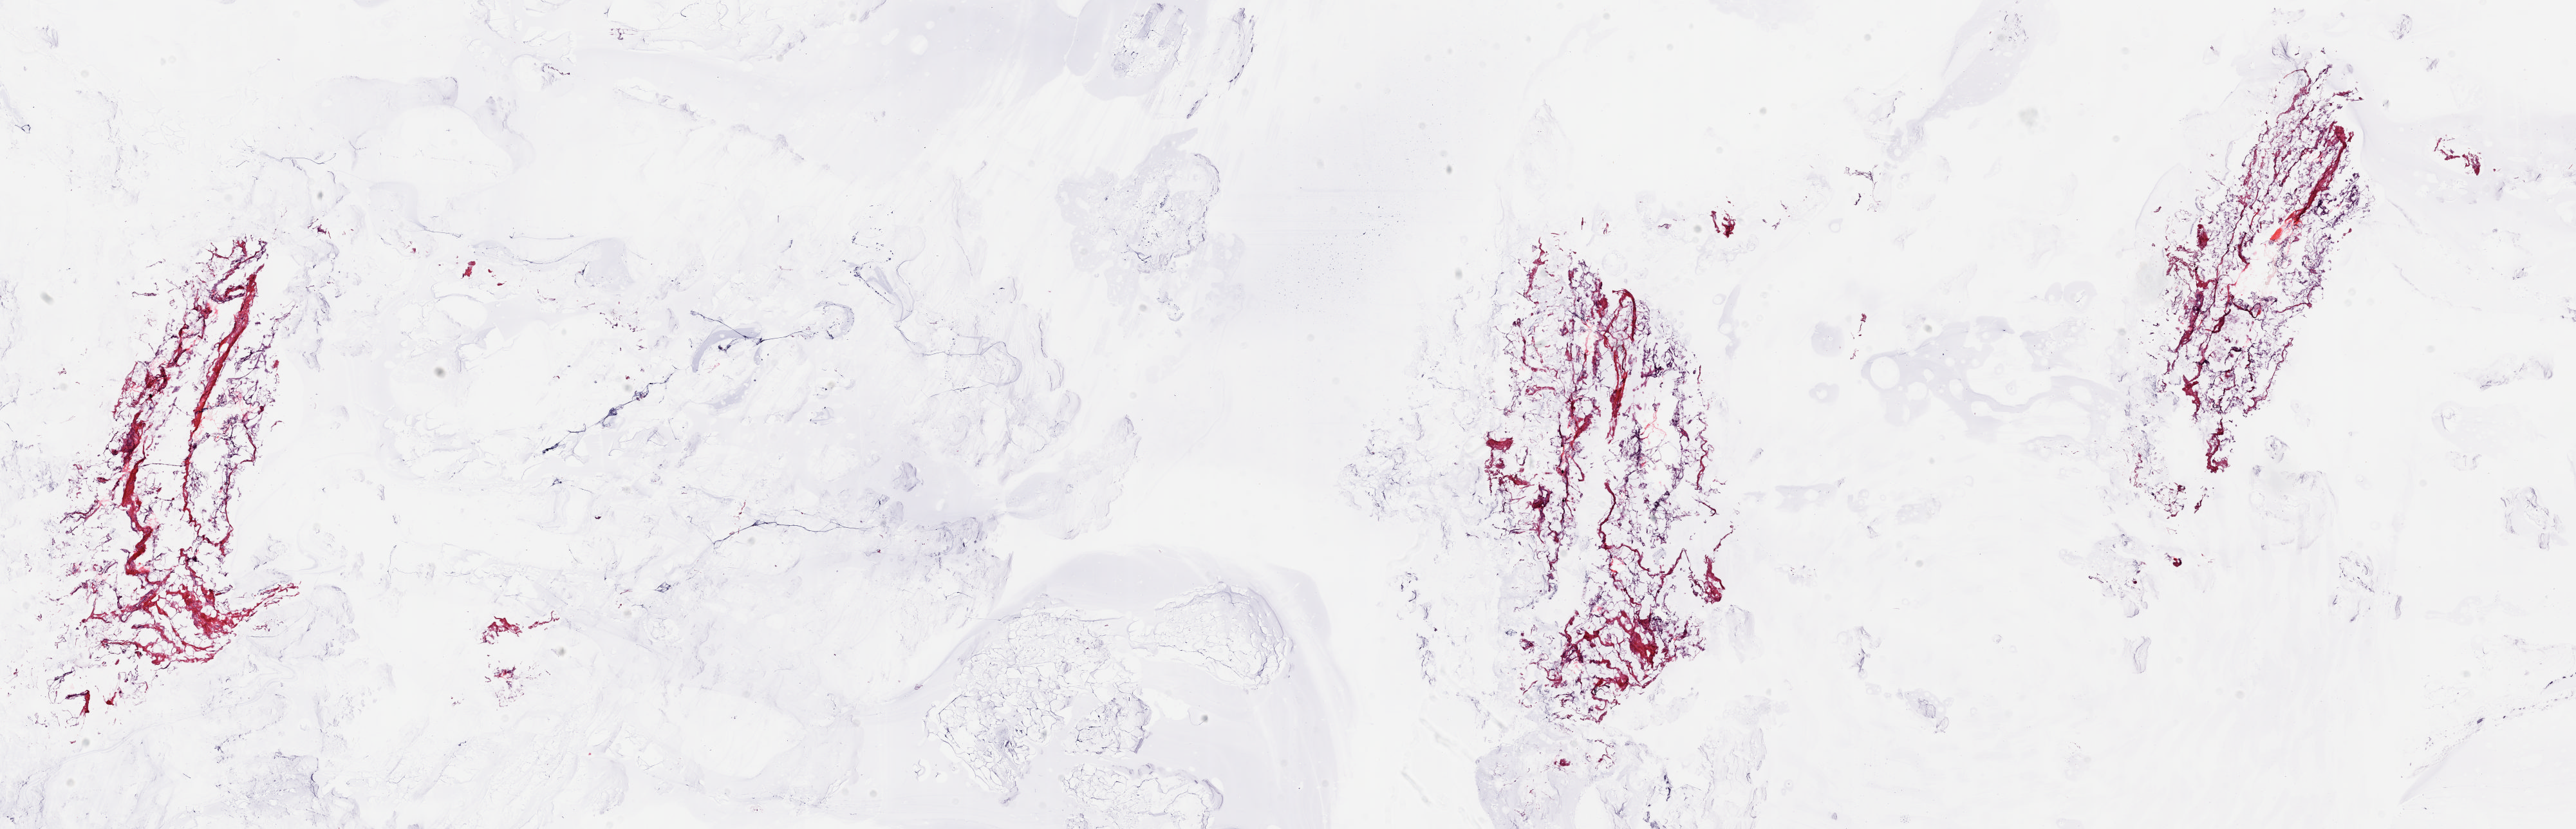
H&E-stained whole-slide image, low-resolution overview of the scanned area, about 31.7 x 10.2 mm (acquisition: 20x scan). Frozen section from the bottom of the tissue portion. Solid tissue normal (non-tumour tissue) sample from the breast. Patient: female, age at initial diagnosis 84 years. Slide review estimates, as recorded: tumour cells 0%, tumour nuclei 0%, normal cells 100%, stromal cells 0%, necrosis 0%. Infiltration values recorded for this section: lymphocyte infiltration 1%, monocyte infiltration 0%, neutrophil infiltration 0%.
* this section: solid tissue normal sample (biorepository sample class)
* patient diagnosis: Infiltrating duct carcinoma, NOS